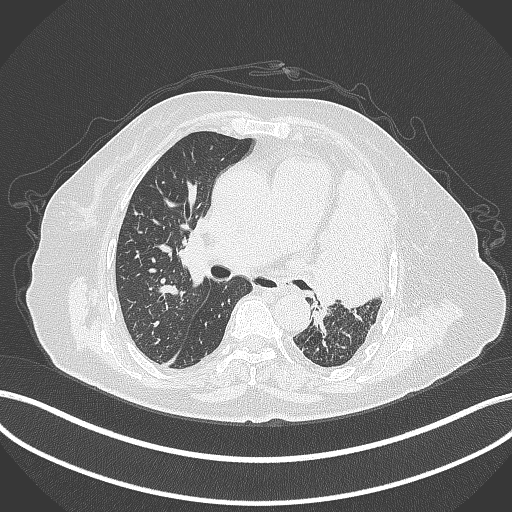
Chest CT, one axial slice. Position 220 of 399 along the scan axis. 120 kVp. Lung window (W 1500 / L -600 HU). 1 mm slice thickness. 512 × 512 image matrix, field of view 400 × 400 mm. Female patient, age 75 years. Case-level facts recorded for this patient, not image findings: clinical TNM (as recorded): T3 N3 M1.
Annotated regions visible in this slice (bounding box drawn by a radiologist):
- lung tumour (recorded histology: adenocarcinoma): bounding box <305,164,393,309> (left, top, right, bottom; pixels)